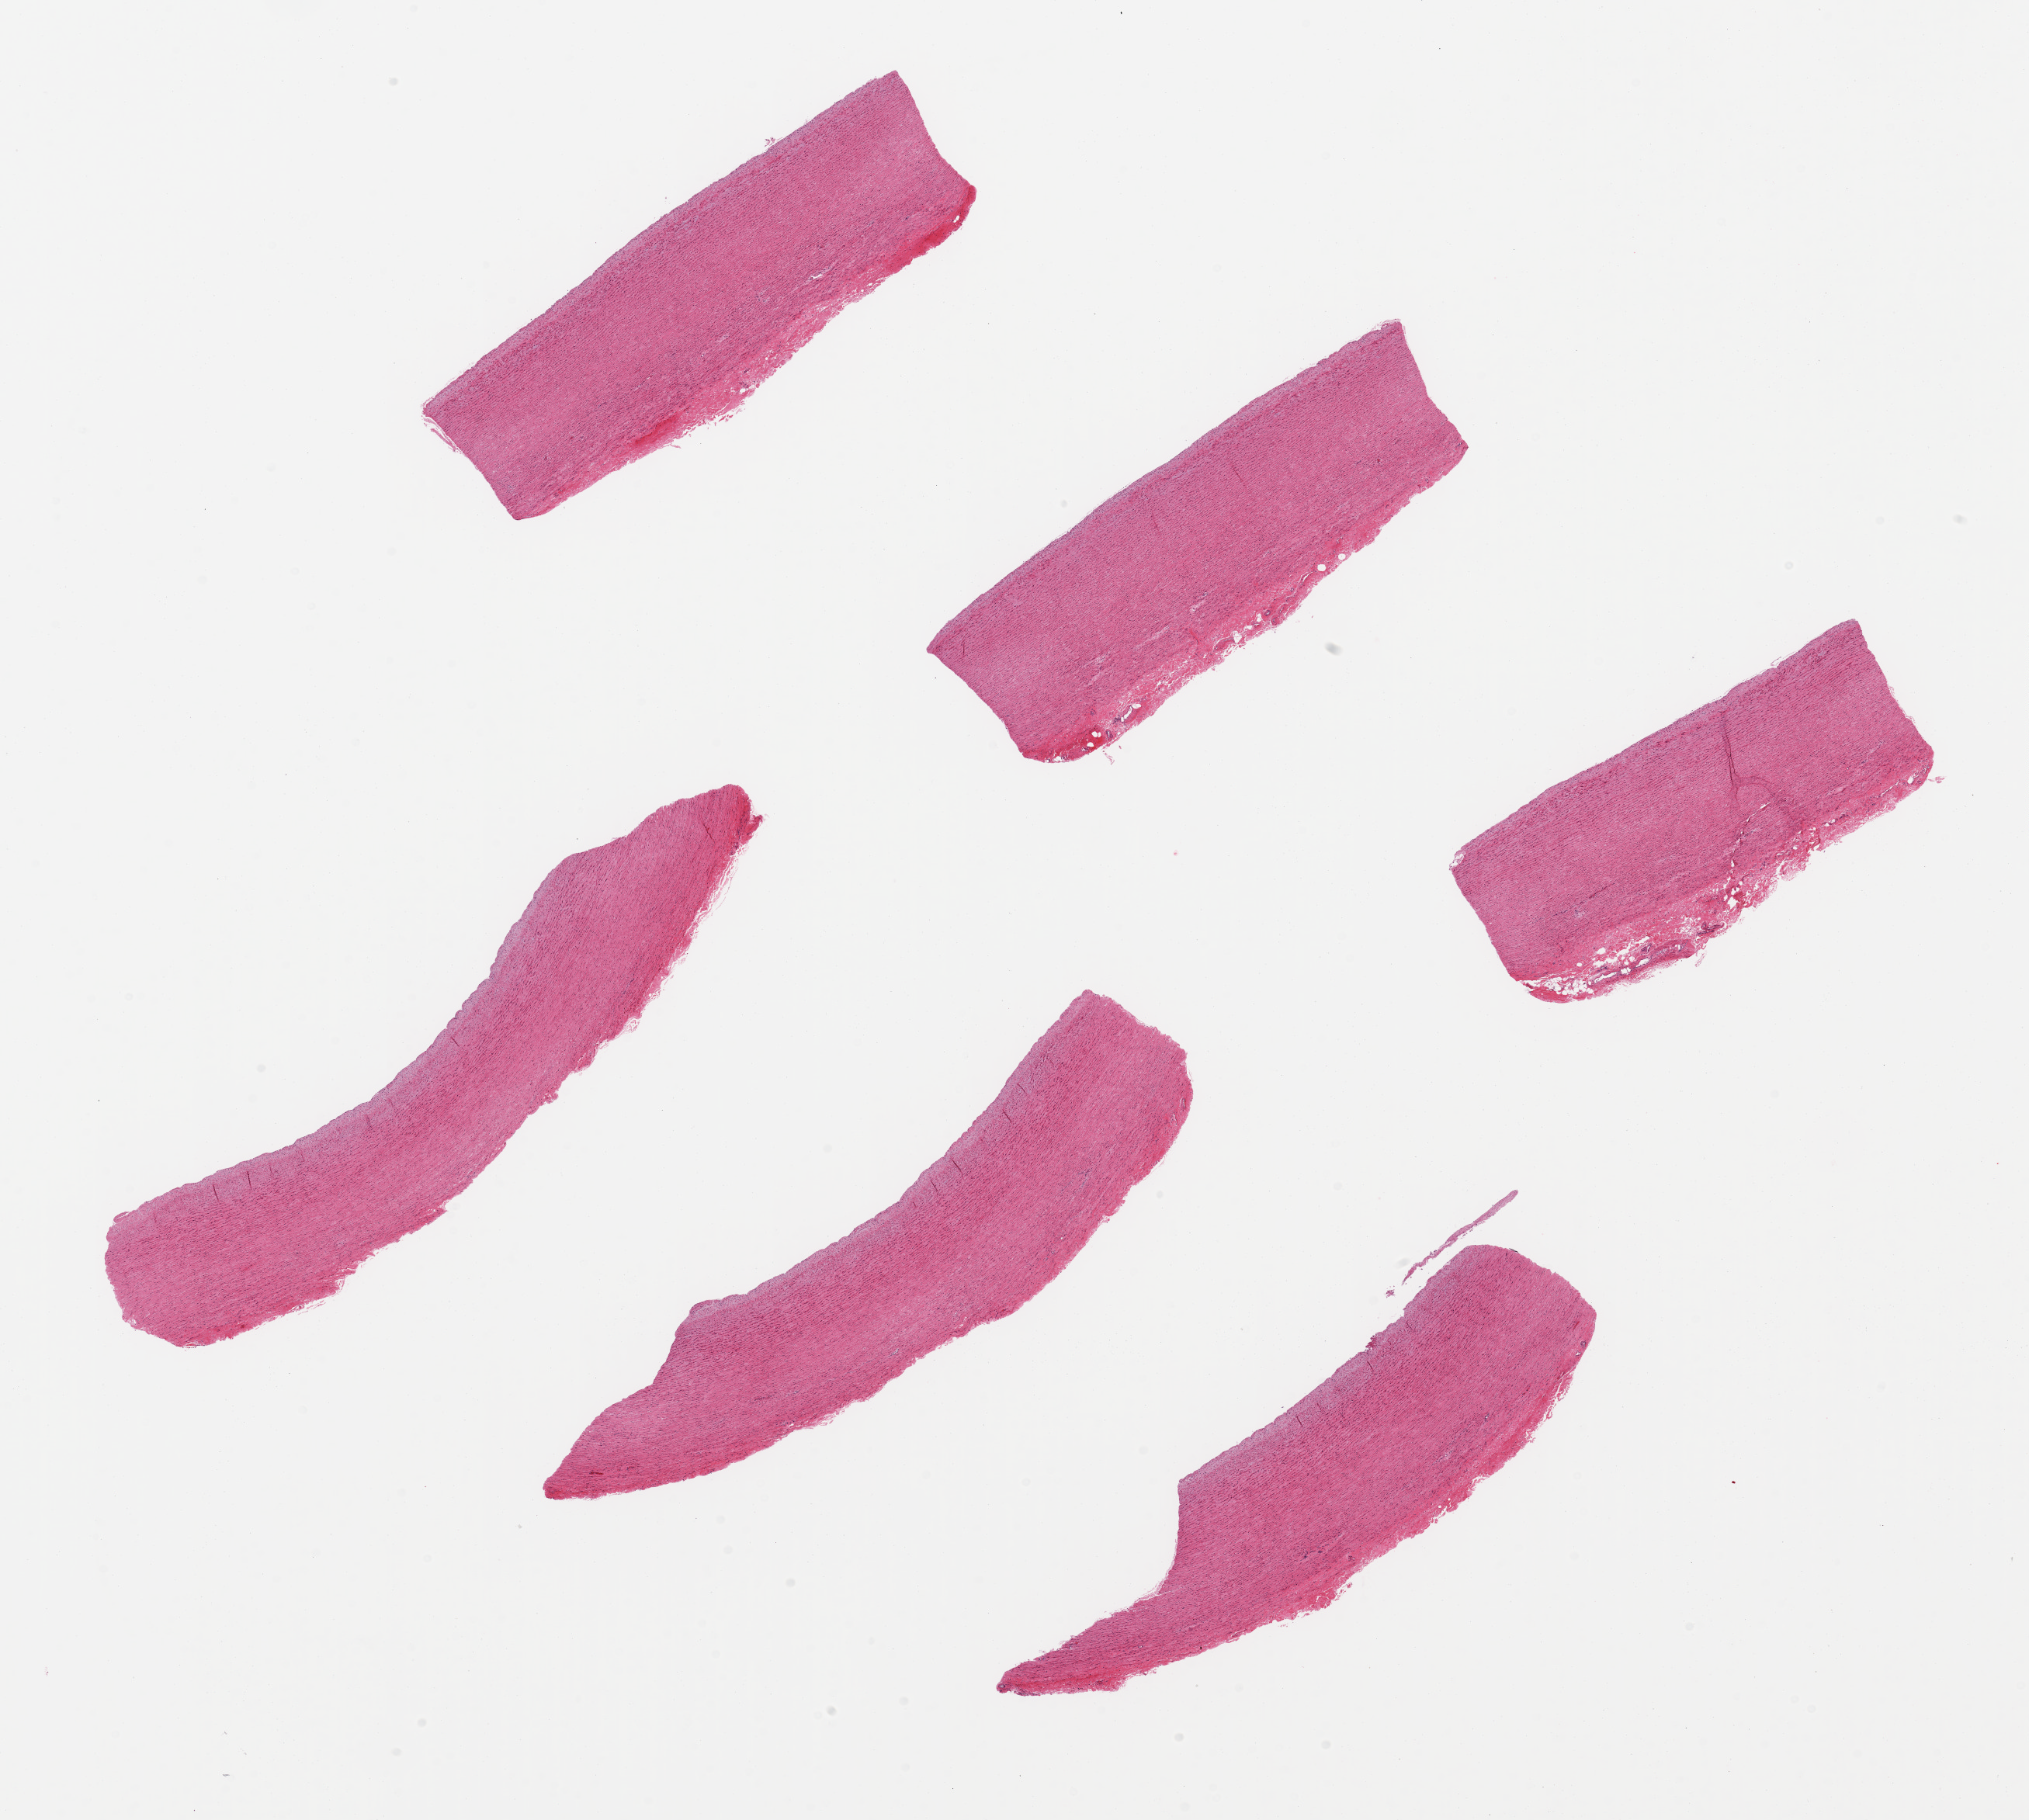
Hematoxylin and eosin (H&E) whole-slide image, brightfield — shown as a low-resolution overview of the whole scanned area (about 20.7 x 18.5 mm, from a 20x scan), PAXgene-fixed, paraffin-embedded tissue, target tissue: aorta, donor tissue sample. Donor sex: female.
Pathologist's review note for this sample: 6 pieces; no plaques; well dissected.